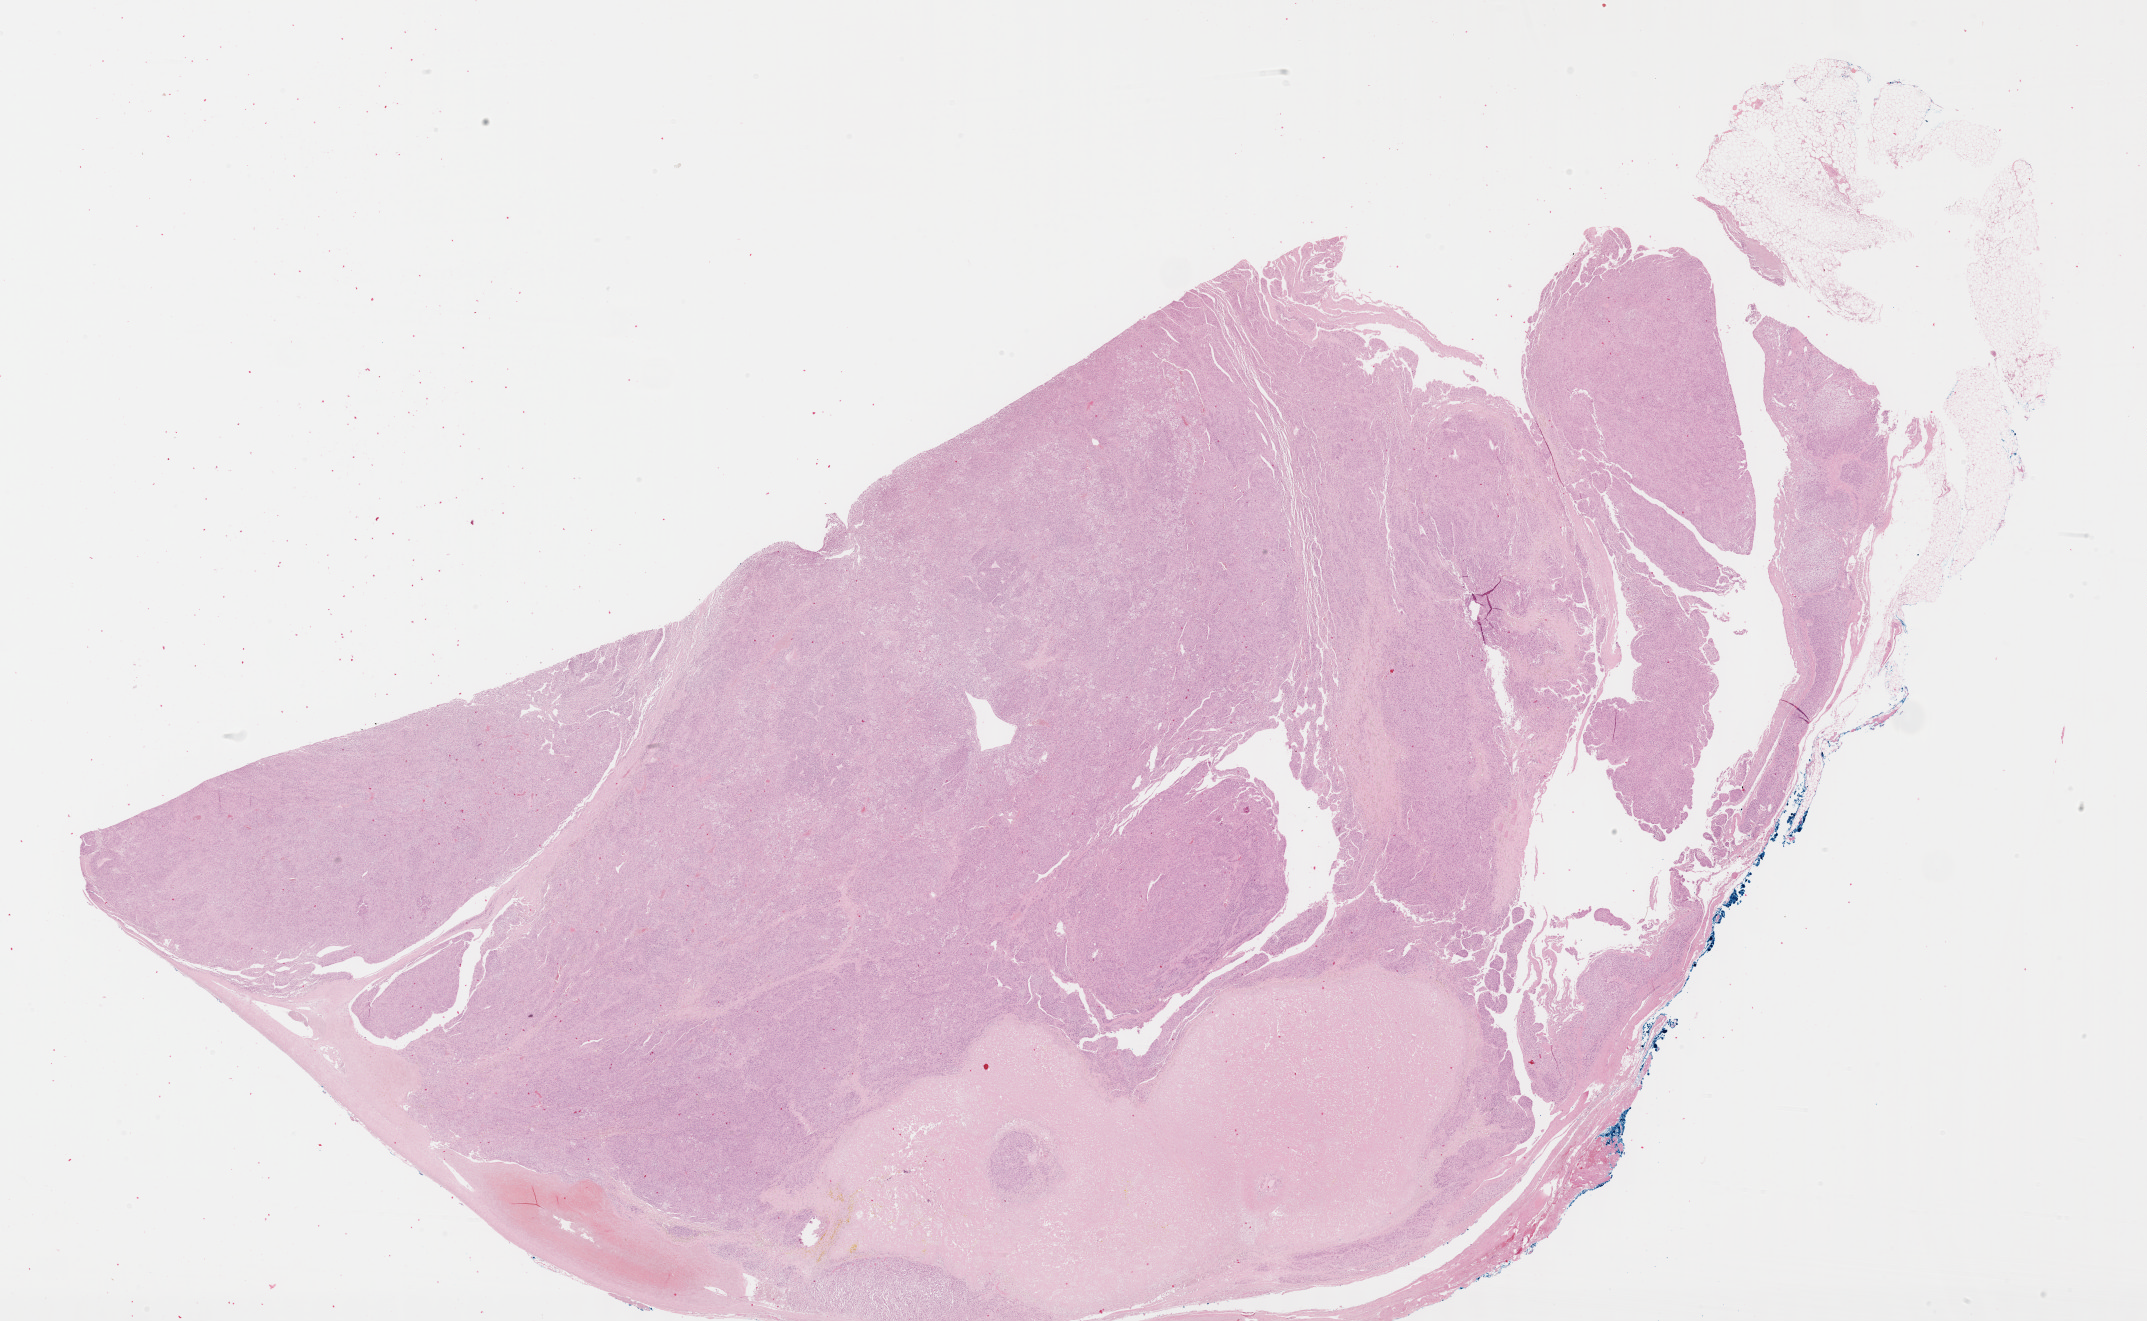
Whole-slide histology image, Hematoxylin and eosin (H&E) stained — a low-resolution overview of the entire scanned area, about 34.7 x 21.4 mm (from a 40x scan); formalin-fixed paraffin-embedded (FFPE) diagnostic section; sample: primary tumour, adrenal cortex. Female, age 17 years at initial diagnosis.
Diagnosis: Adrenal cortical carcinoma (cortex of adrenal gland). Laterality: left.